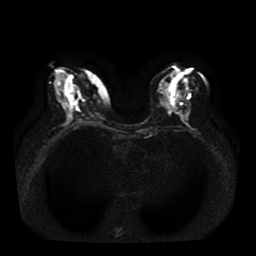
Breast MRI, one axial slice. Slice 17 of 41 in the series (ordered by position). Diffusion-weighted series; image 2 of 4 stored at this slice position (different b-values; order by instance number). 1.5 T. 5 mm slice thickness. 256 × 256 image matrix, field of view 330 × 330 mm. Female patient.
Structures marked on this image (expert manual segmentation):
- tumour on diffusion-weighted imaging: bounding box [x1, y1, x2, y2] px = [72, 93, 81, 103]